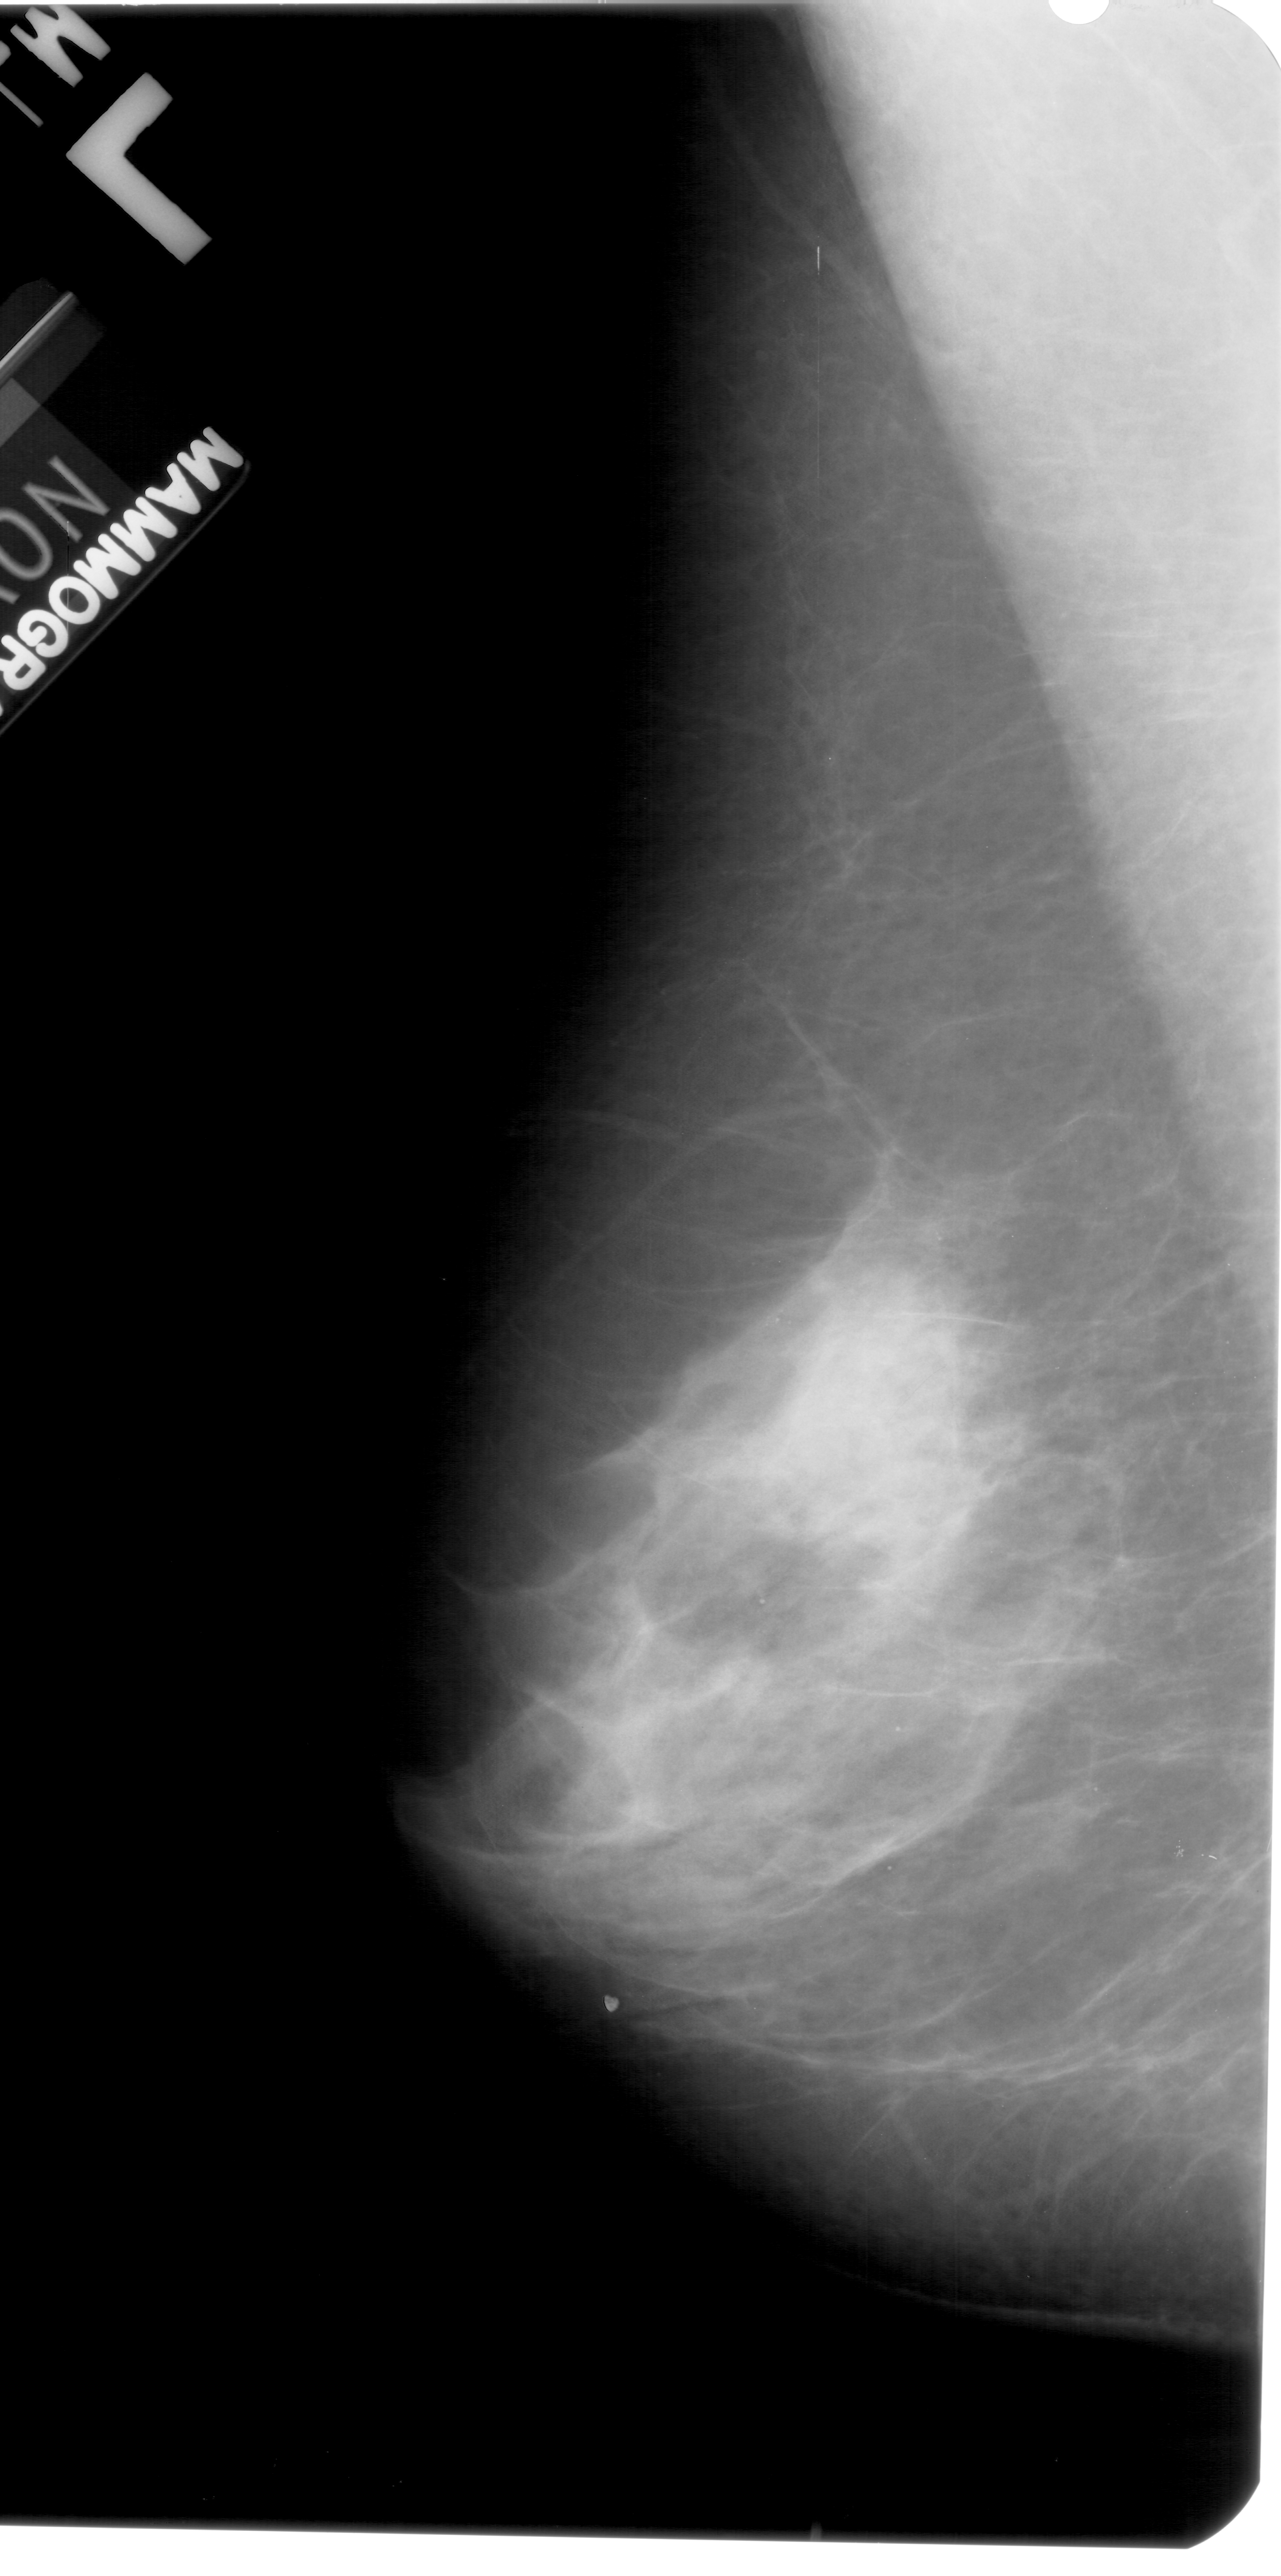
Digitized screen-film mammogram. Left breast. MLO view. BI-RADS breast density category 4 (scale 1–4). 1281 × 2576 image matrix.
Marked abnormalities (boxes around the expert regions of interest):
- calcifications, morphology pleomorphic, distribution clustered; BI-RADS assessment category 4; pathology result (as recorded, not read from the image): benign: bounding box (x1, y1, x2, y2) in pixels: (724, 1255, 865, 1391)